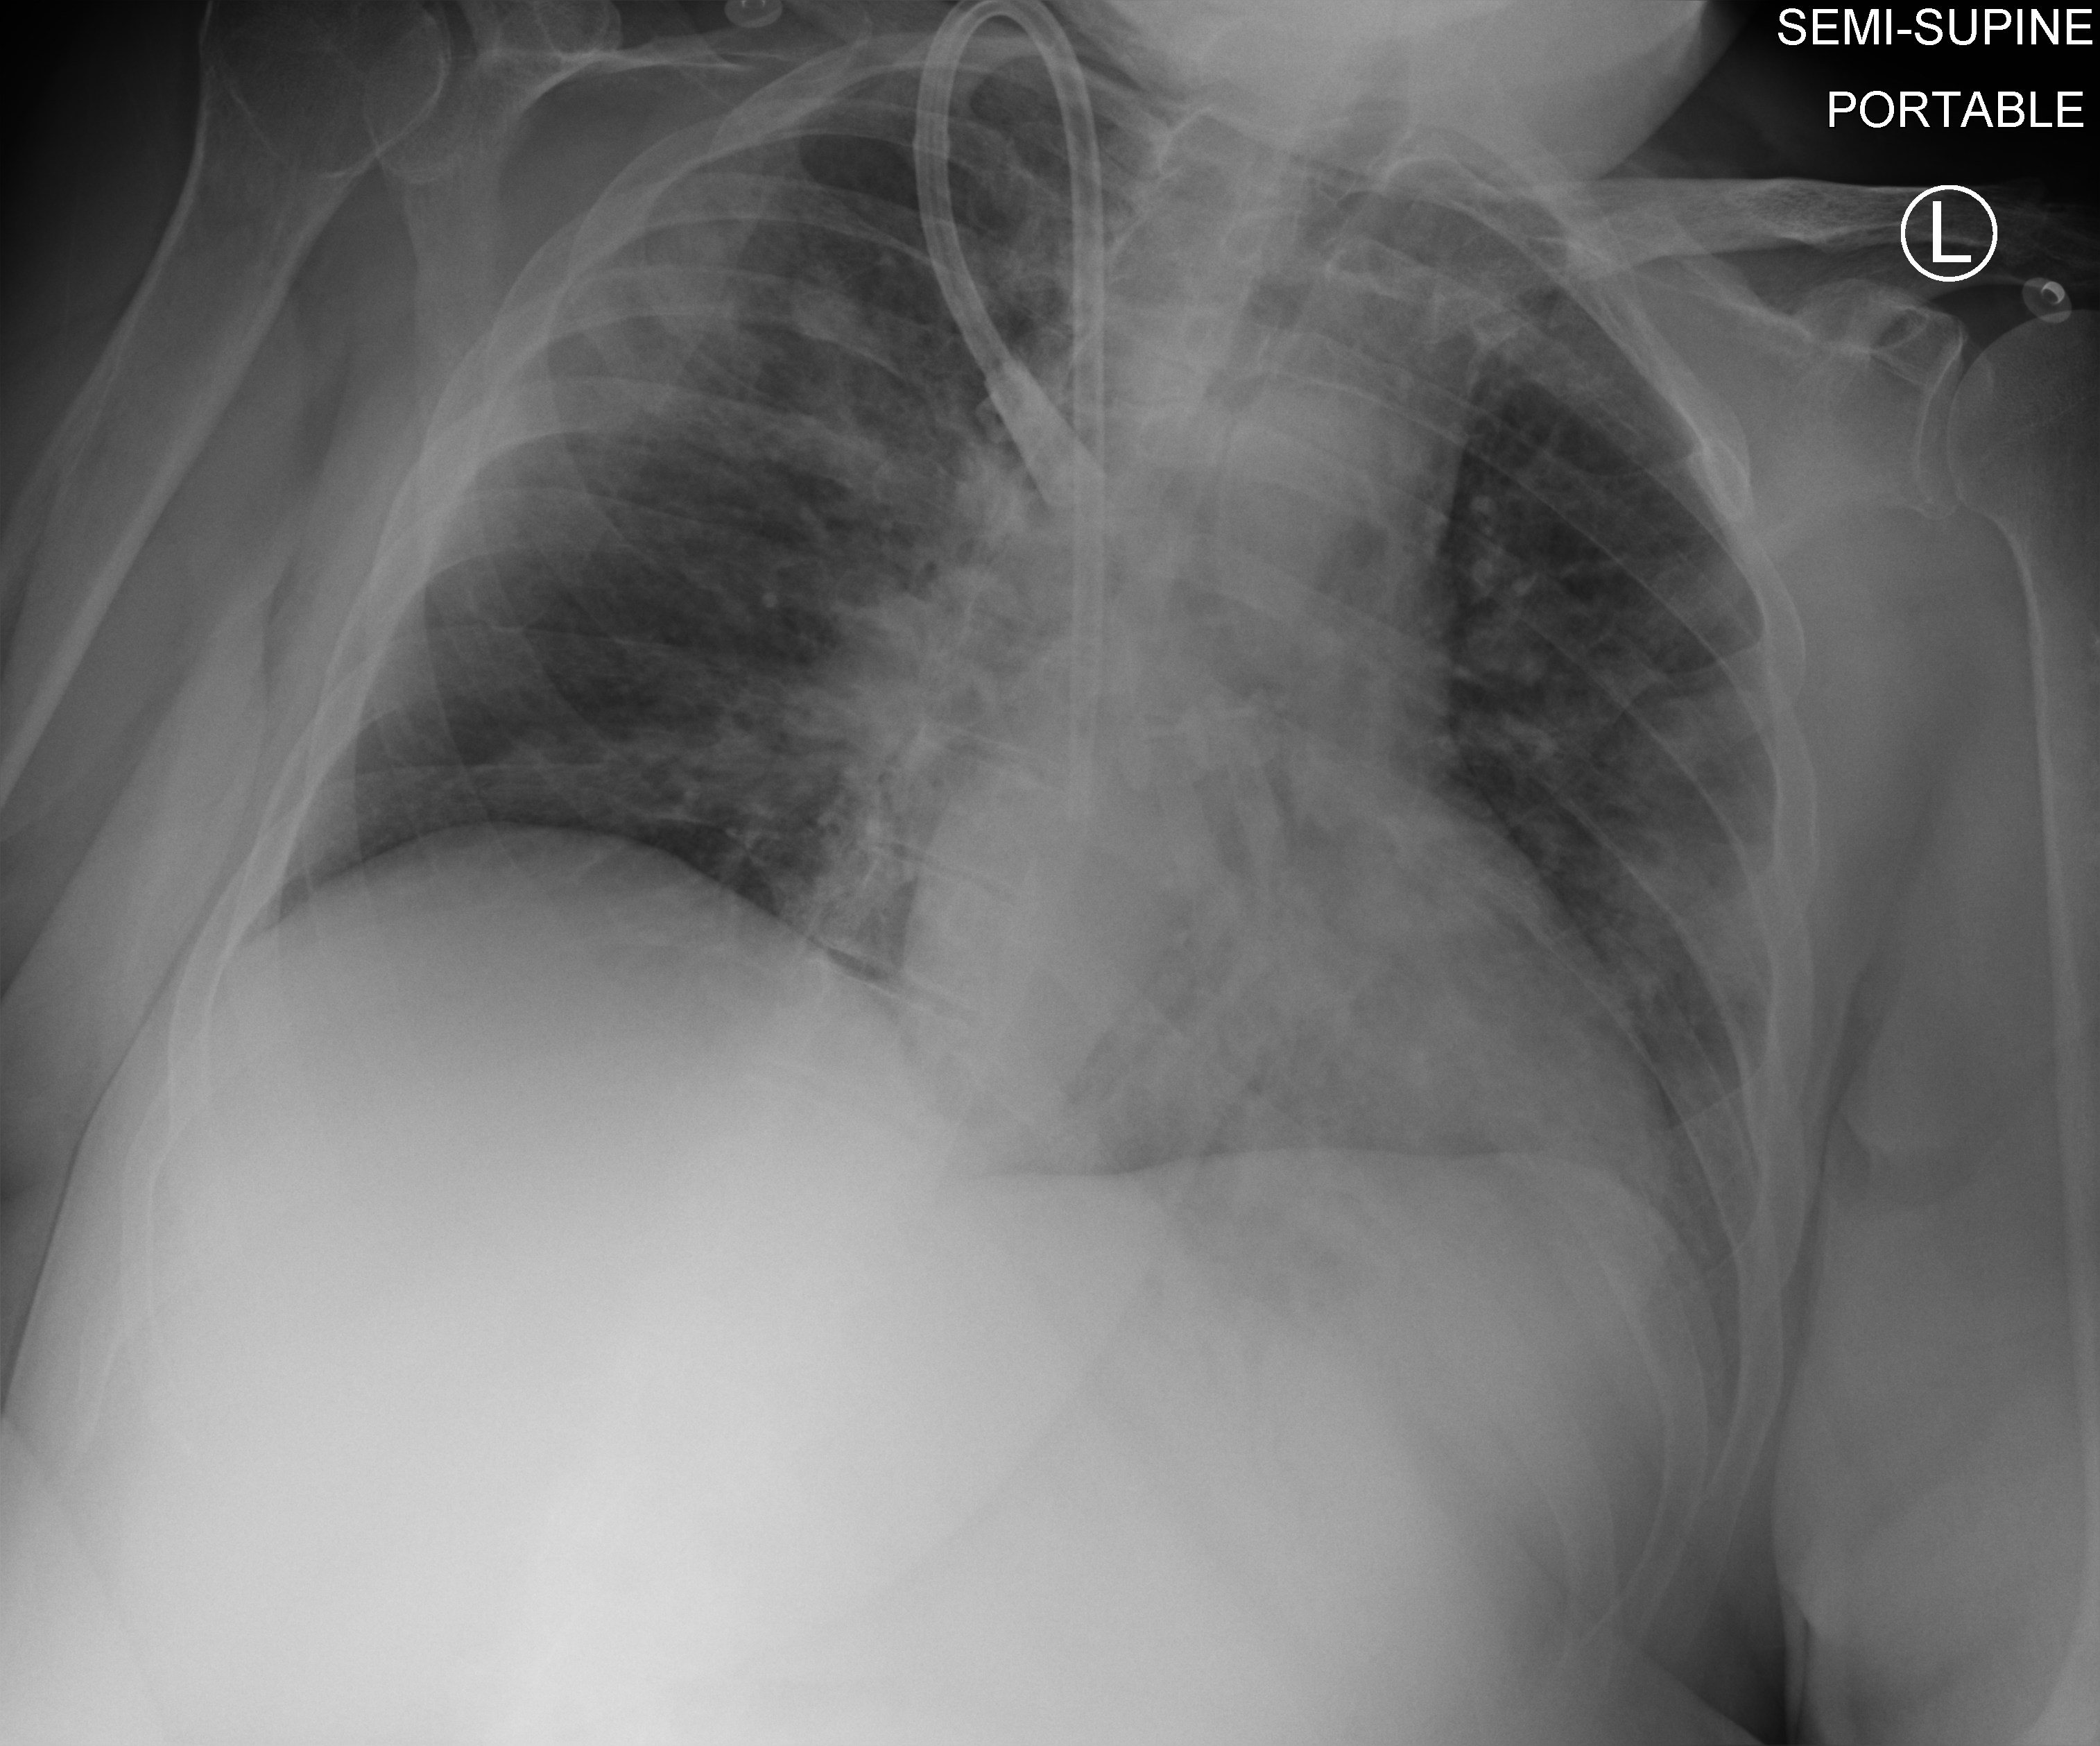
Portable chest radiograph; anteroposterior (AP) projection. Female patient hospitalised with COVID-19, age 60–74 years.
Hospital-stay facts (about this admission, not read from this image; timing relative to this image not recorded): mechanically ventilated during this hospital stay: no.